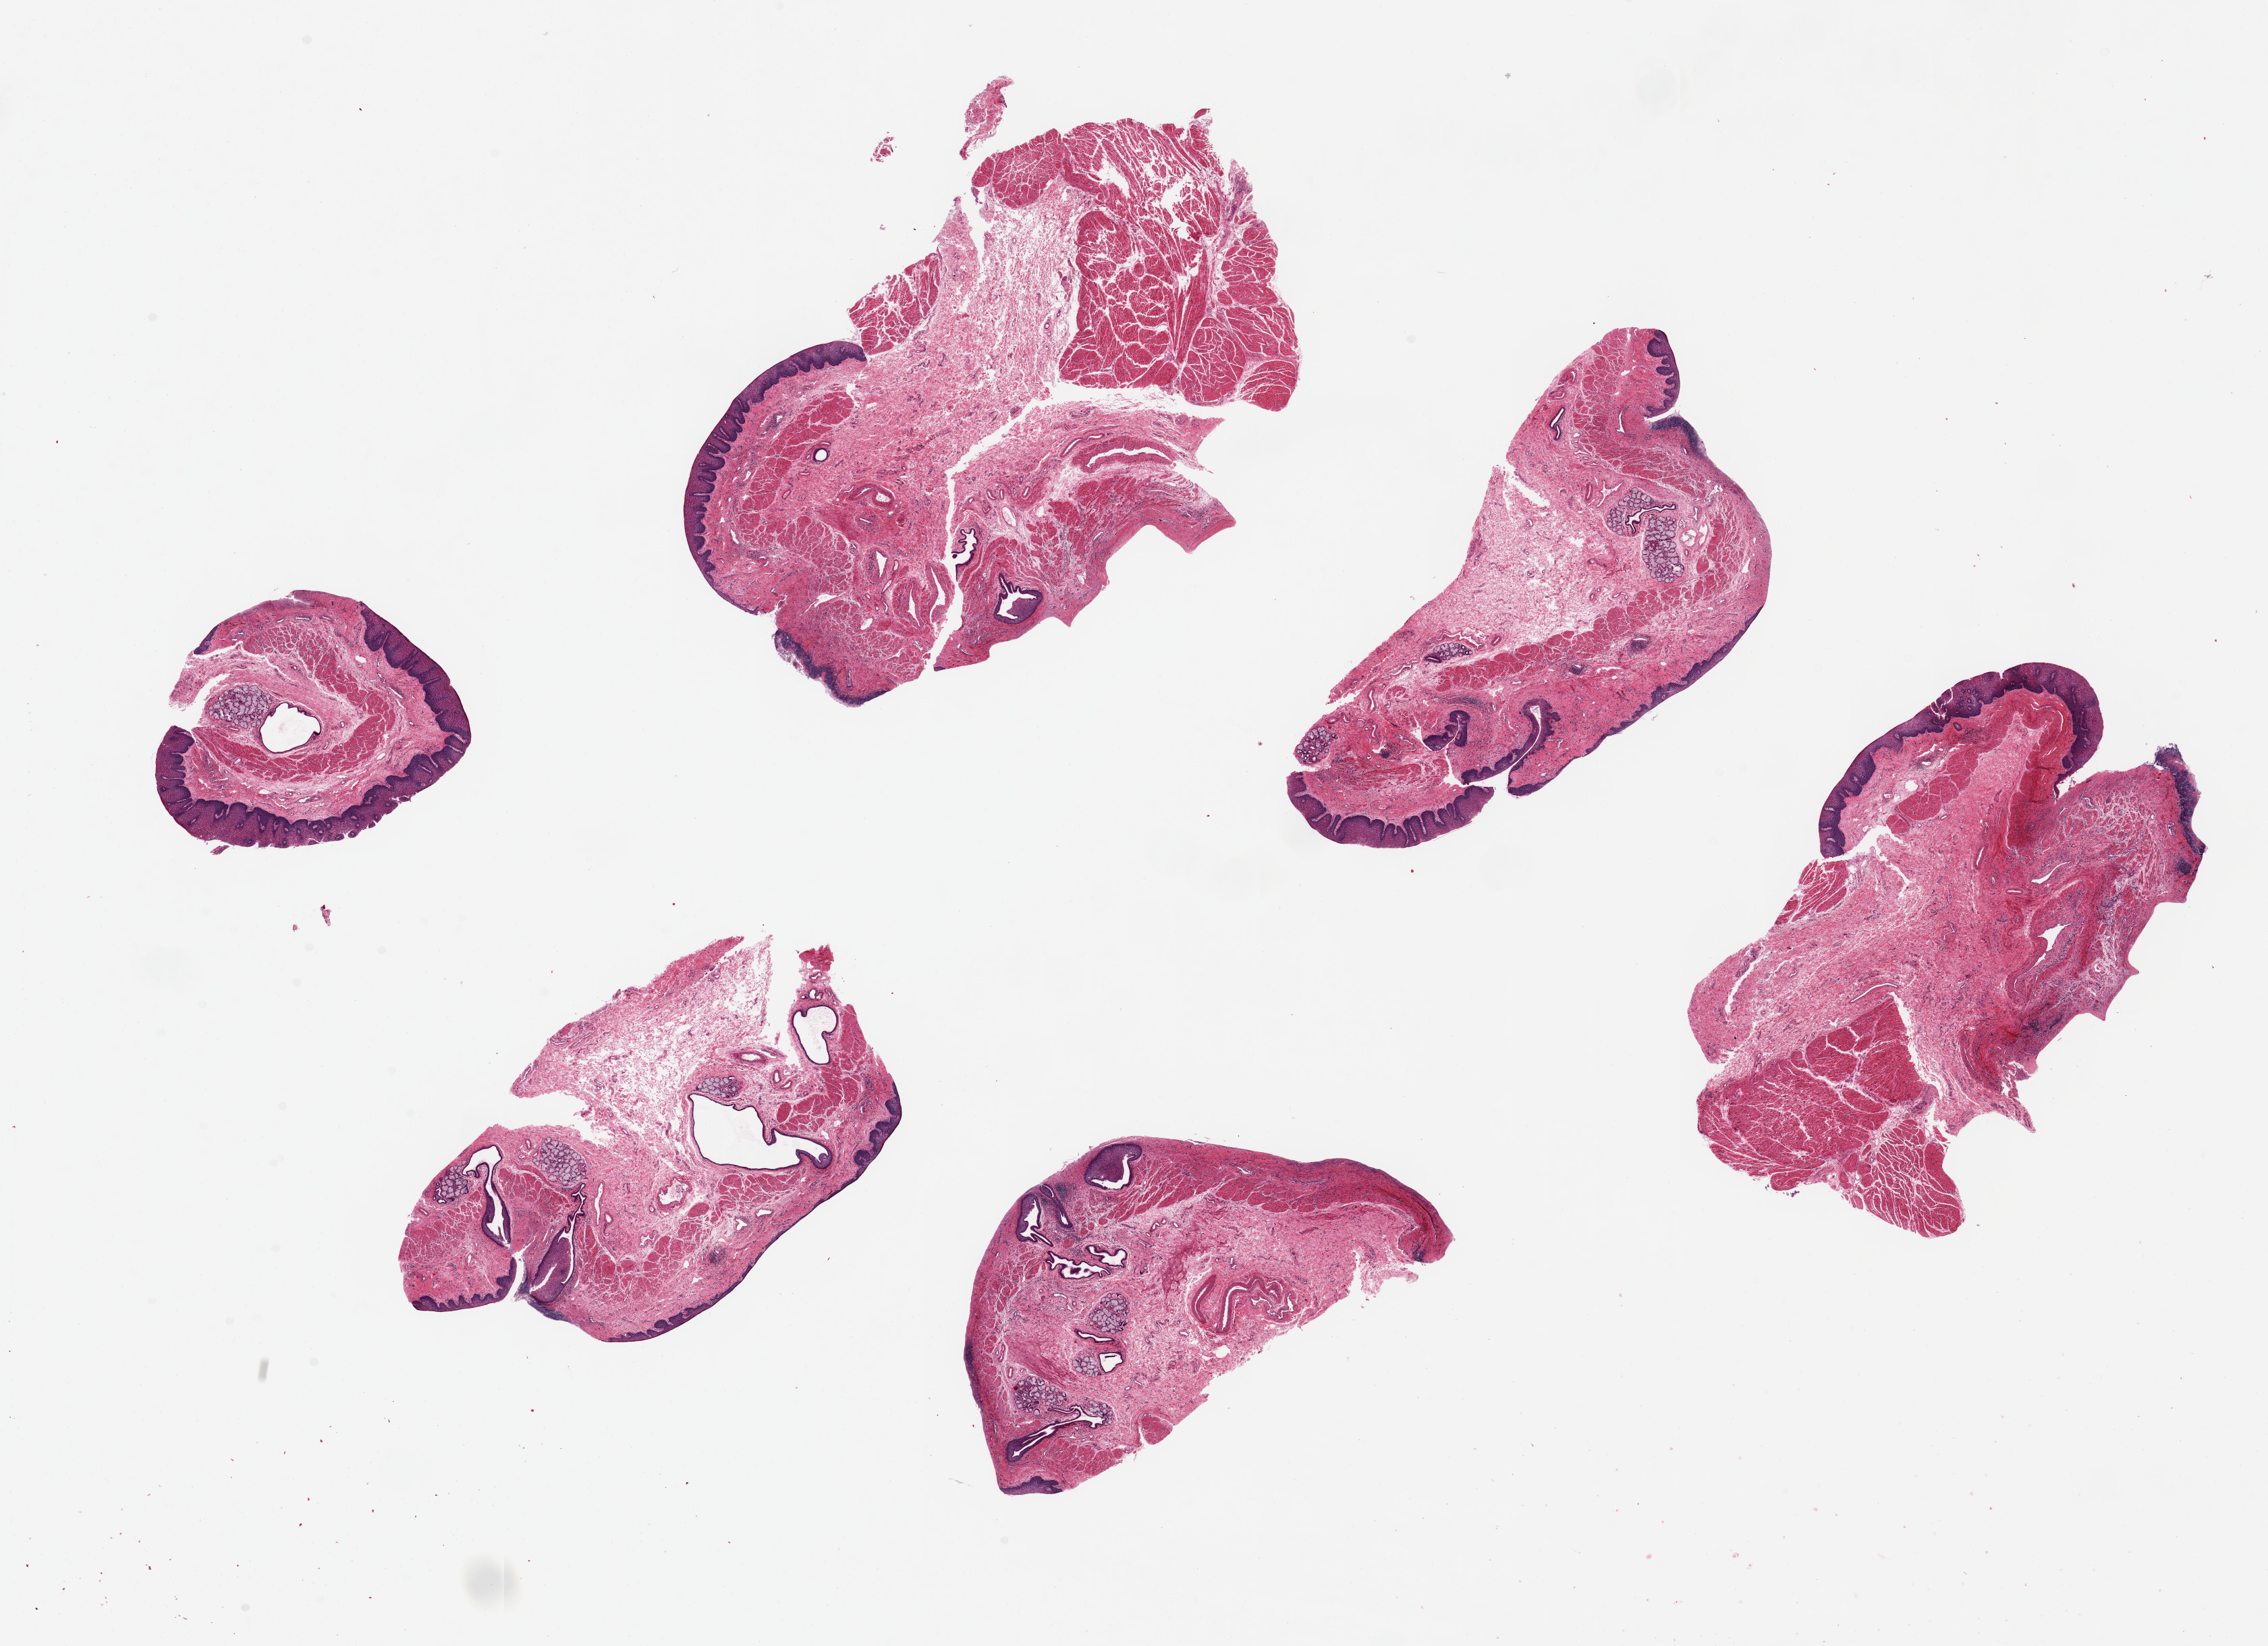
H&E whole-slide image, a low-resolution overview of the entire scanned area, about 26.6 x 19.3 mm (from a 20x scan), PAXgene-fixed paraffin-embedded (PFPE) section, sampled site (target tissue): esophageal mucous membrane, donor tissue sample. Donor sex: female.
• review note (as recorded): 6 ~6.5x3mm pieces. Squamous mucosa is 5-10% of thickness